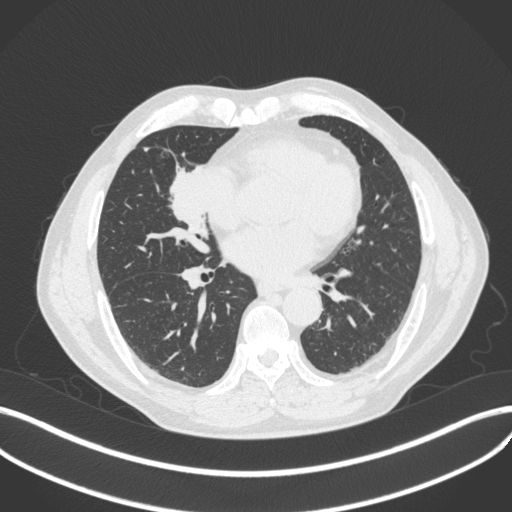
Chest CT, one axial slice; position 180 of 429 along the scan axis; reconstruction kernel B31f; 120 kVp; lung window (W 1500 / L -600 HU); 1 mm slice thickness; 512 × 512 image matrix, field of view 400 × 400 mm. Male patient, age 61 years. From the clinical record (not read from this slice): clinical TNM (as recorded): T2b N1 M0.
Outlined on this slice (rectangle marked by the reading radiologist):
- lung tumour (recorded histology: squamous cell carcinoma): box from (x=166, y=150) to (x=222, y=242) px